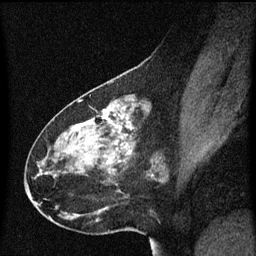
Breast MRI (dynamic contrast-enhanced), one sagittal slice; position 27 of 60 along the scan axis; dynamic contrast-enhanced series, image 2 of 3 at this slice position (ordered by acquisition); 1.5 T; TE 4.2 ms, TR 8.4 ms; 2 mm slice thickness; 256 × 256 image matrix, field of view 200 × 200 mm. Patient: female, 49 years. Case-level facts recorded for this patient, not image findings: setting: breast cancer imaged before/during neoadjuvant chemotherapy; receptor status: HR-positive, HER2-negative.
Structures marked on this image (semi-automatic segmentation, software-assisted and operator-edited):
- analysis volume of interest (the breast-tissue region the enhancement analysis was run in; not a lesion): bounding box (x1, y1, x2, y2) in pixels: (27, 96, 170, 221)
- tumour enhancement mask (voxels above the 70 % enhancement threshold inside the analysis volume of interest): (105, 110, 129, 163)